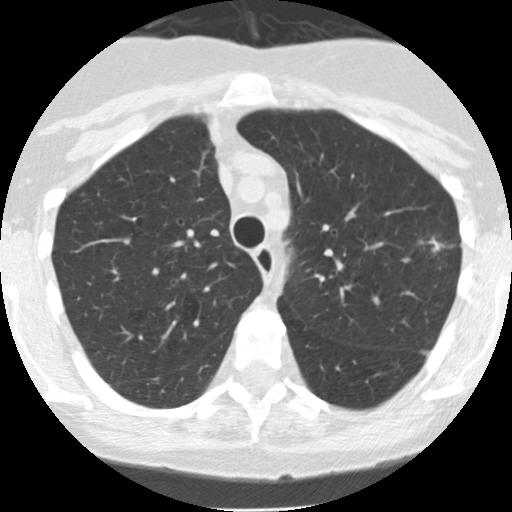
Low-dose screening chest CT, one axial slice. Position 110 of 145 along the scan axis. Reconstruction kernel STANDARD. 120 kVp. Lung window (W 1500 / L -600 HU). 2.5 mm slice thickness. 512 × 512 image matrix.
Structures marked on this image (outlined manually by an expert reader):
- lesion 1 (tumor, upper lobe of left lung): bounding box <428,237,445,253> (left, top, right, bottom; pixels)